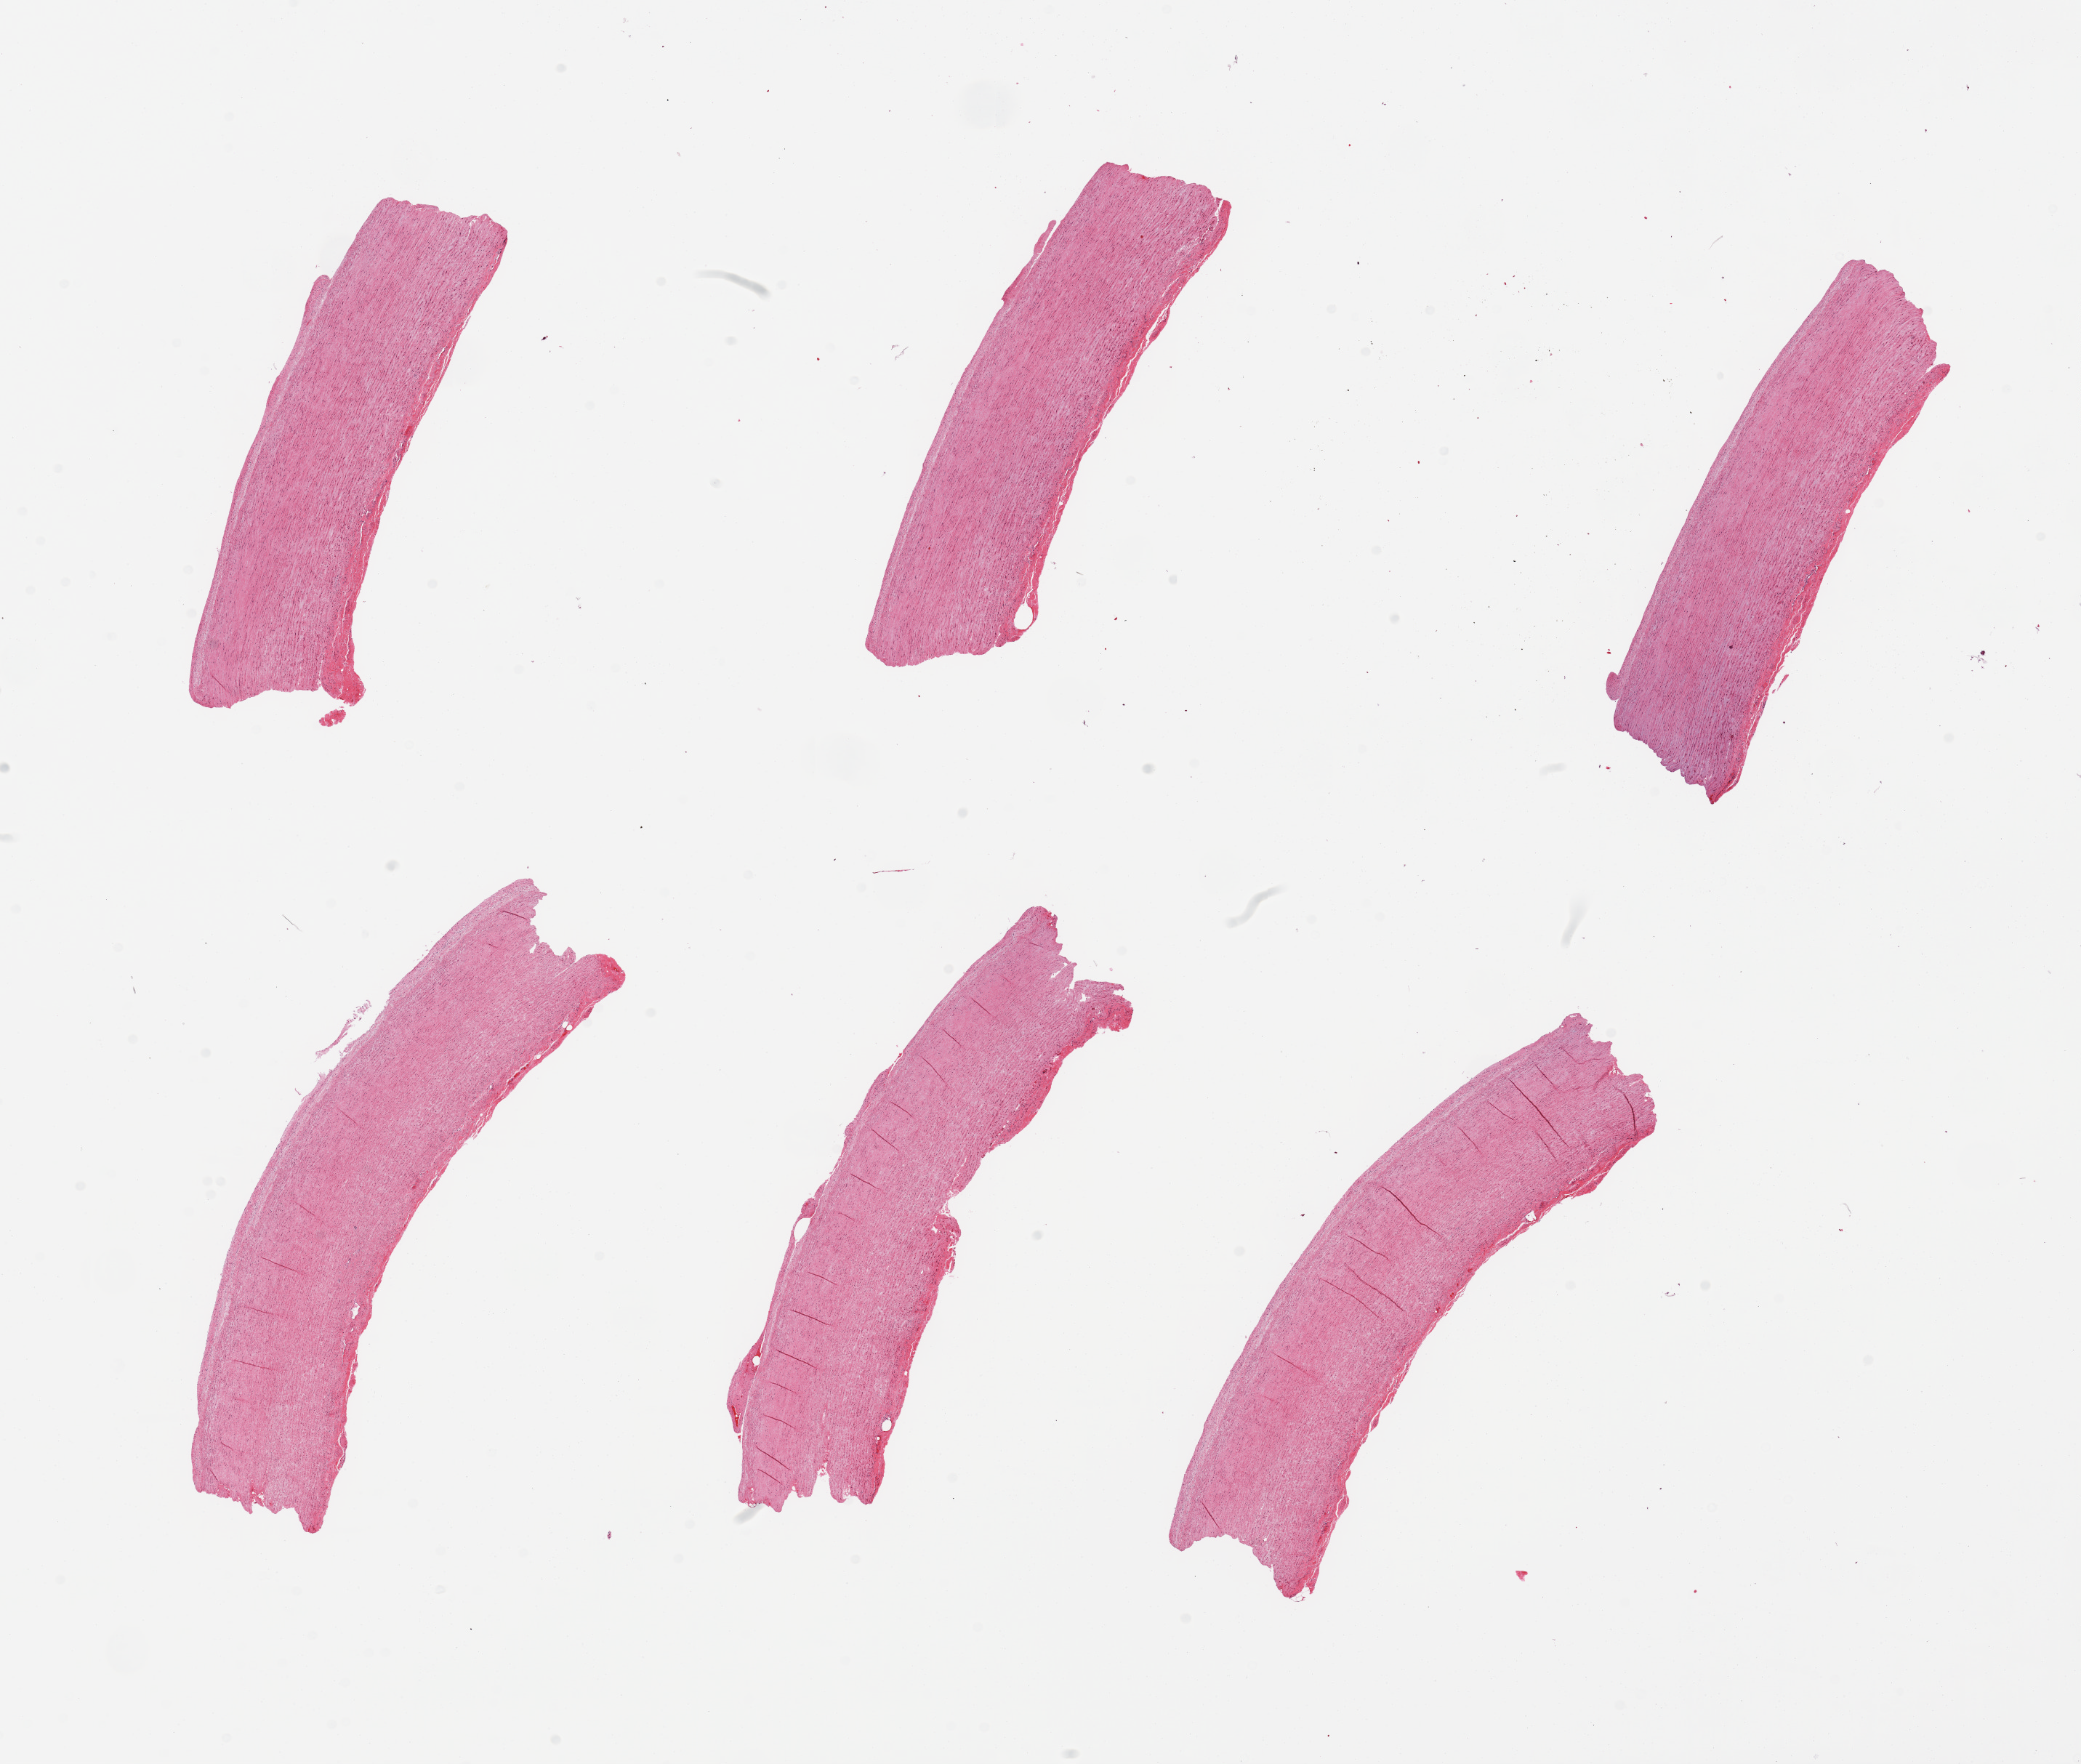
Whole-slide image, hematoxylin and eosin (H&E) stain — shown as a low-resolution overview of the whole scanned area (about 22.6 x 19.2 mm), PAXgene-fixed paraffin-embedded (PFPE) section, target tissue: aorta, donor tissue sample. Donor sex: male.
Reviewer comment on this tissue sample: 6 pieces; minimal plaque.